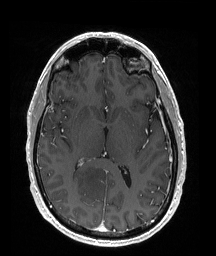
Brain MRI from a brain-tumour surgery series, one axial slice. Position 93 of 176 along the scan axis. T1-weighted post-contrast. 1 mm slice thickness. 216 × 256 image matrix, field of view 211 × 250 mm. Case-level facts recorded for this patient, not image findings: histopathology: Oligodendroglioma; WHO grade: 2; IDH mutation: yes.
Outlined on this slice (outlined manually by an expert reader):
- tumour: box from (x=70, y=162) to (x=111, y=199) px